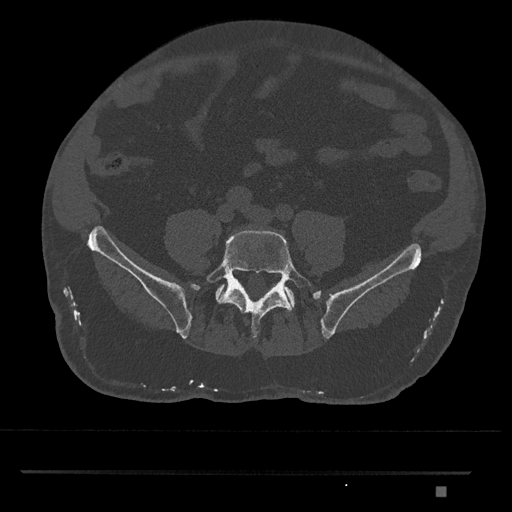
CT including the spine, one axial slice; slice 553 of 1134 in the series (ordered by position); 120 kVp; bone window (W 1800 / L 400 HU); 0.5 mm slice thickness; 512 × 512 image matrix, field of view 429 × 429 mm. Male patient, age 65 years. Case-level facts recorded for this patient, not image findings: primary cancer: prostate.
Annotated regions visible in this slice (semi-automatically segmented with operator editing):
- L5 vertebra: box from (x=206, y=230) to (x=313, y=339) px